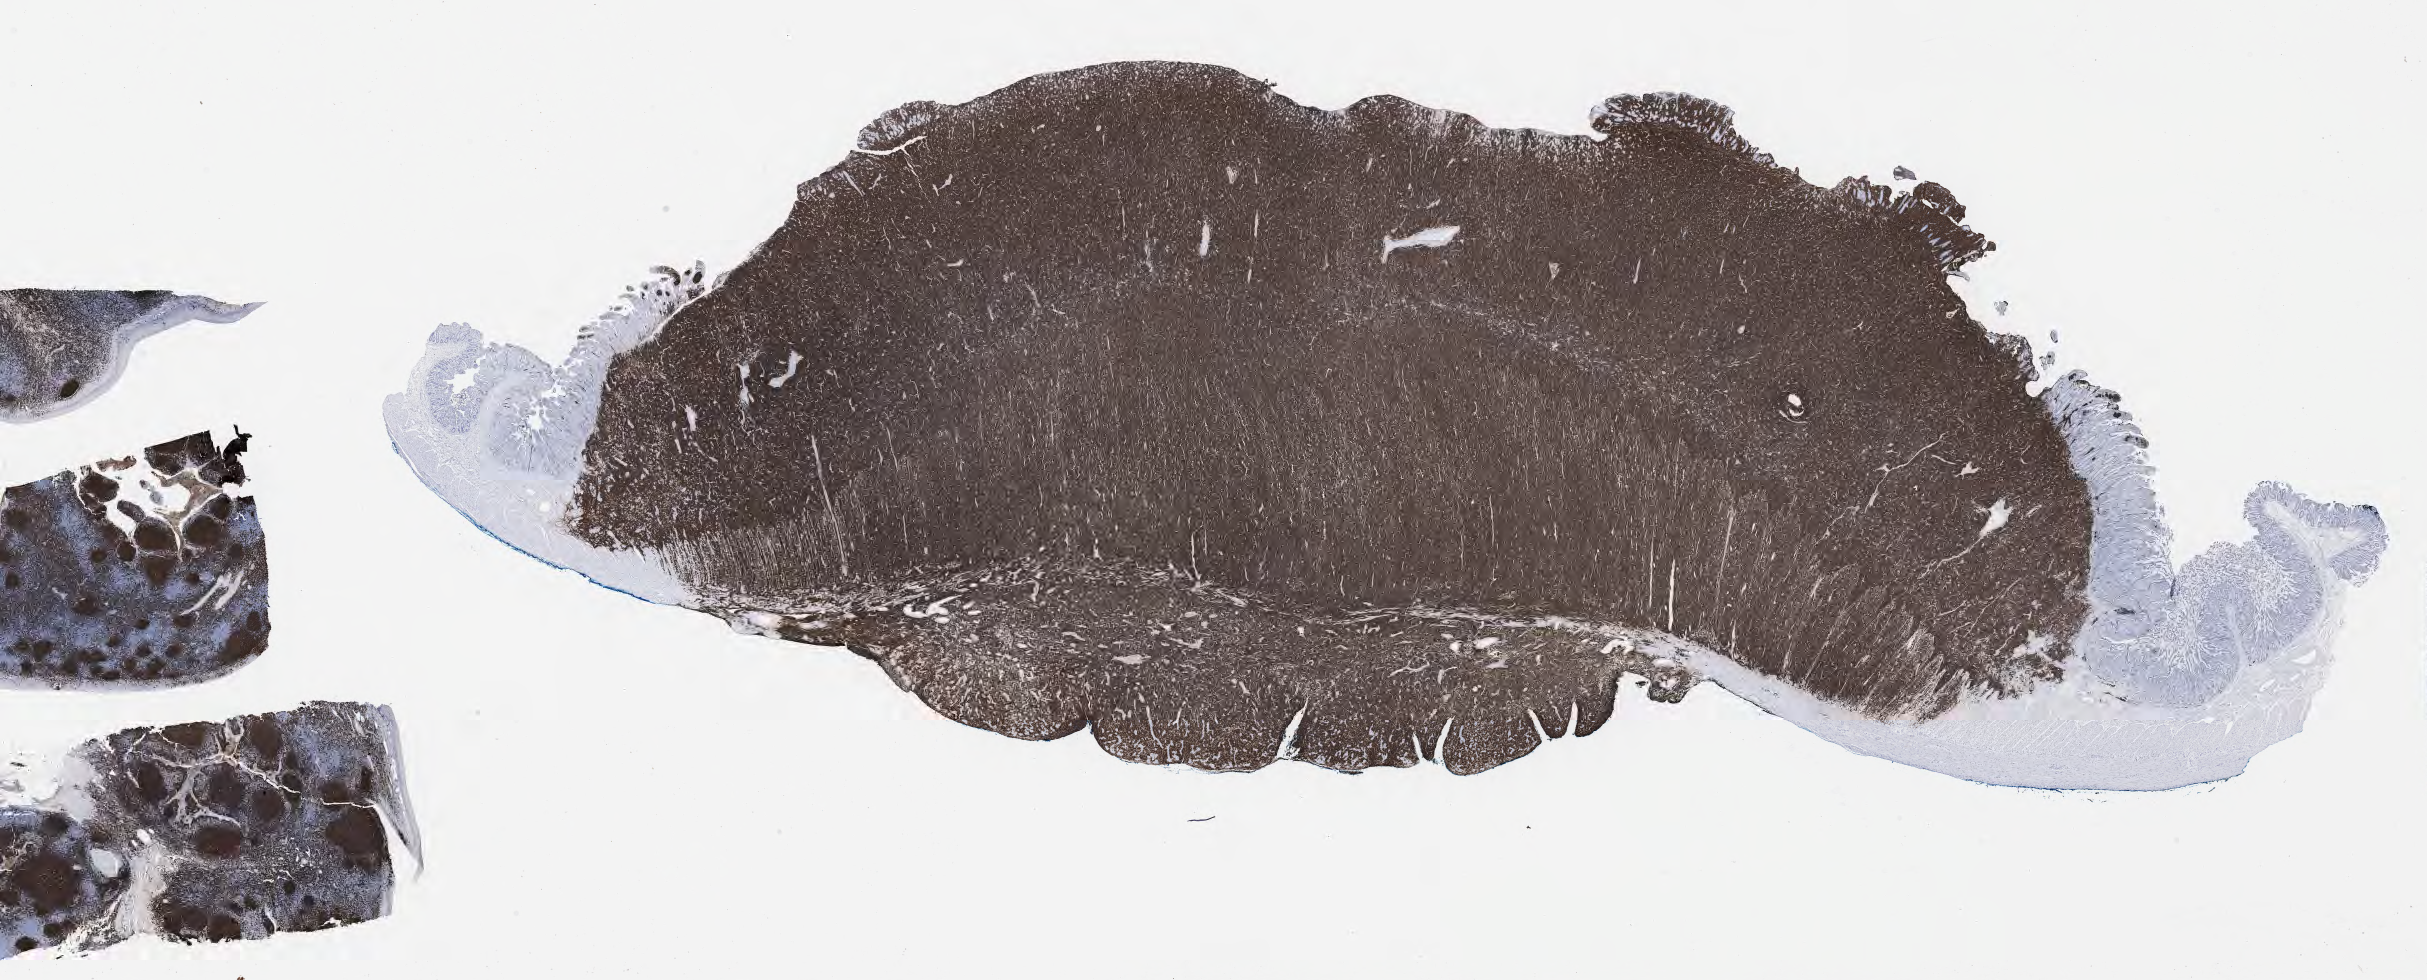
IHC for CD20, whole-slide image, whole scanned area (about 39.2 x 15.8 mm) shown as a low-resolution overview. Specimen: tumor tissue. Anatomic site: small intestine. Male, age 6 years at initial diagnosis.
Histologic diagnosis: Burkitt lymphoma, NOS.